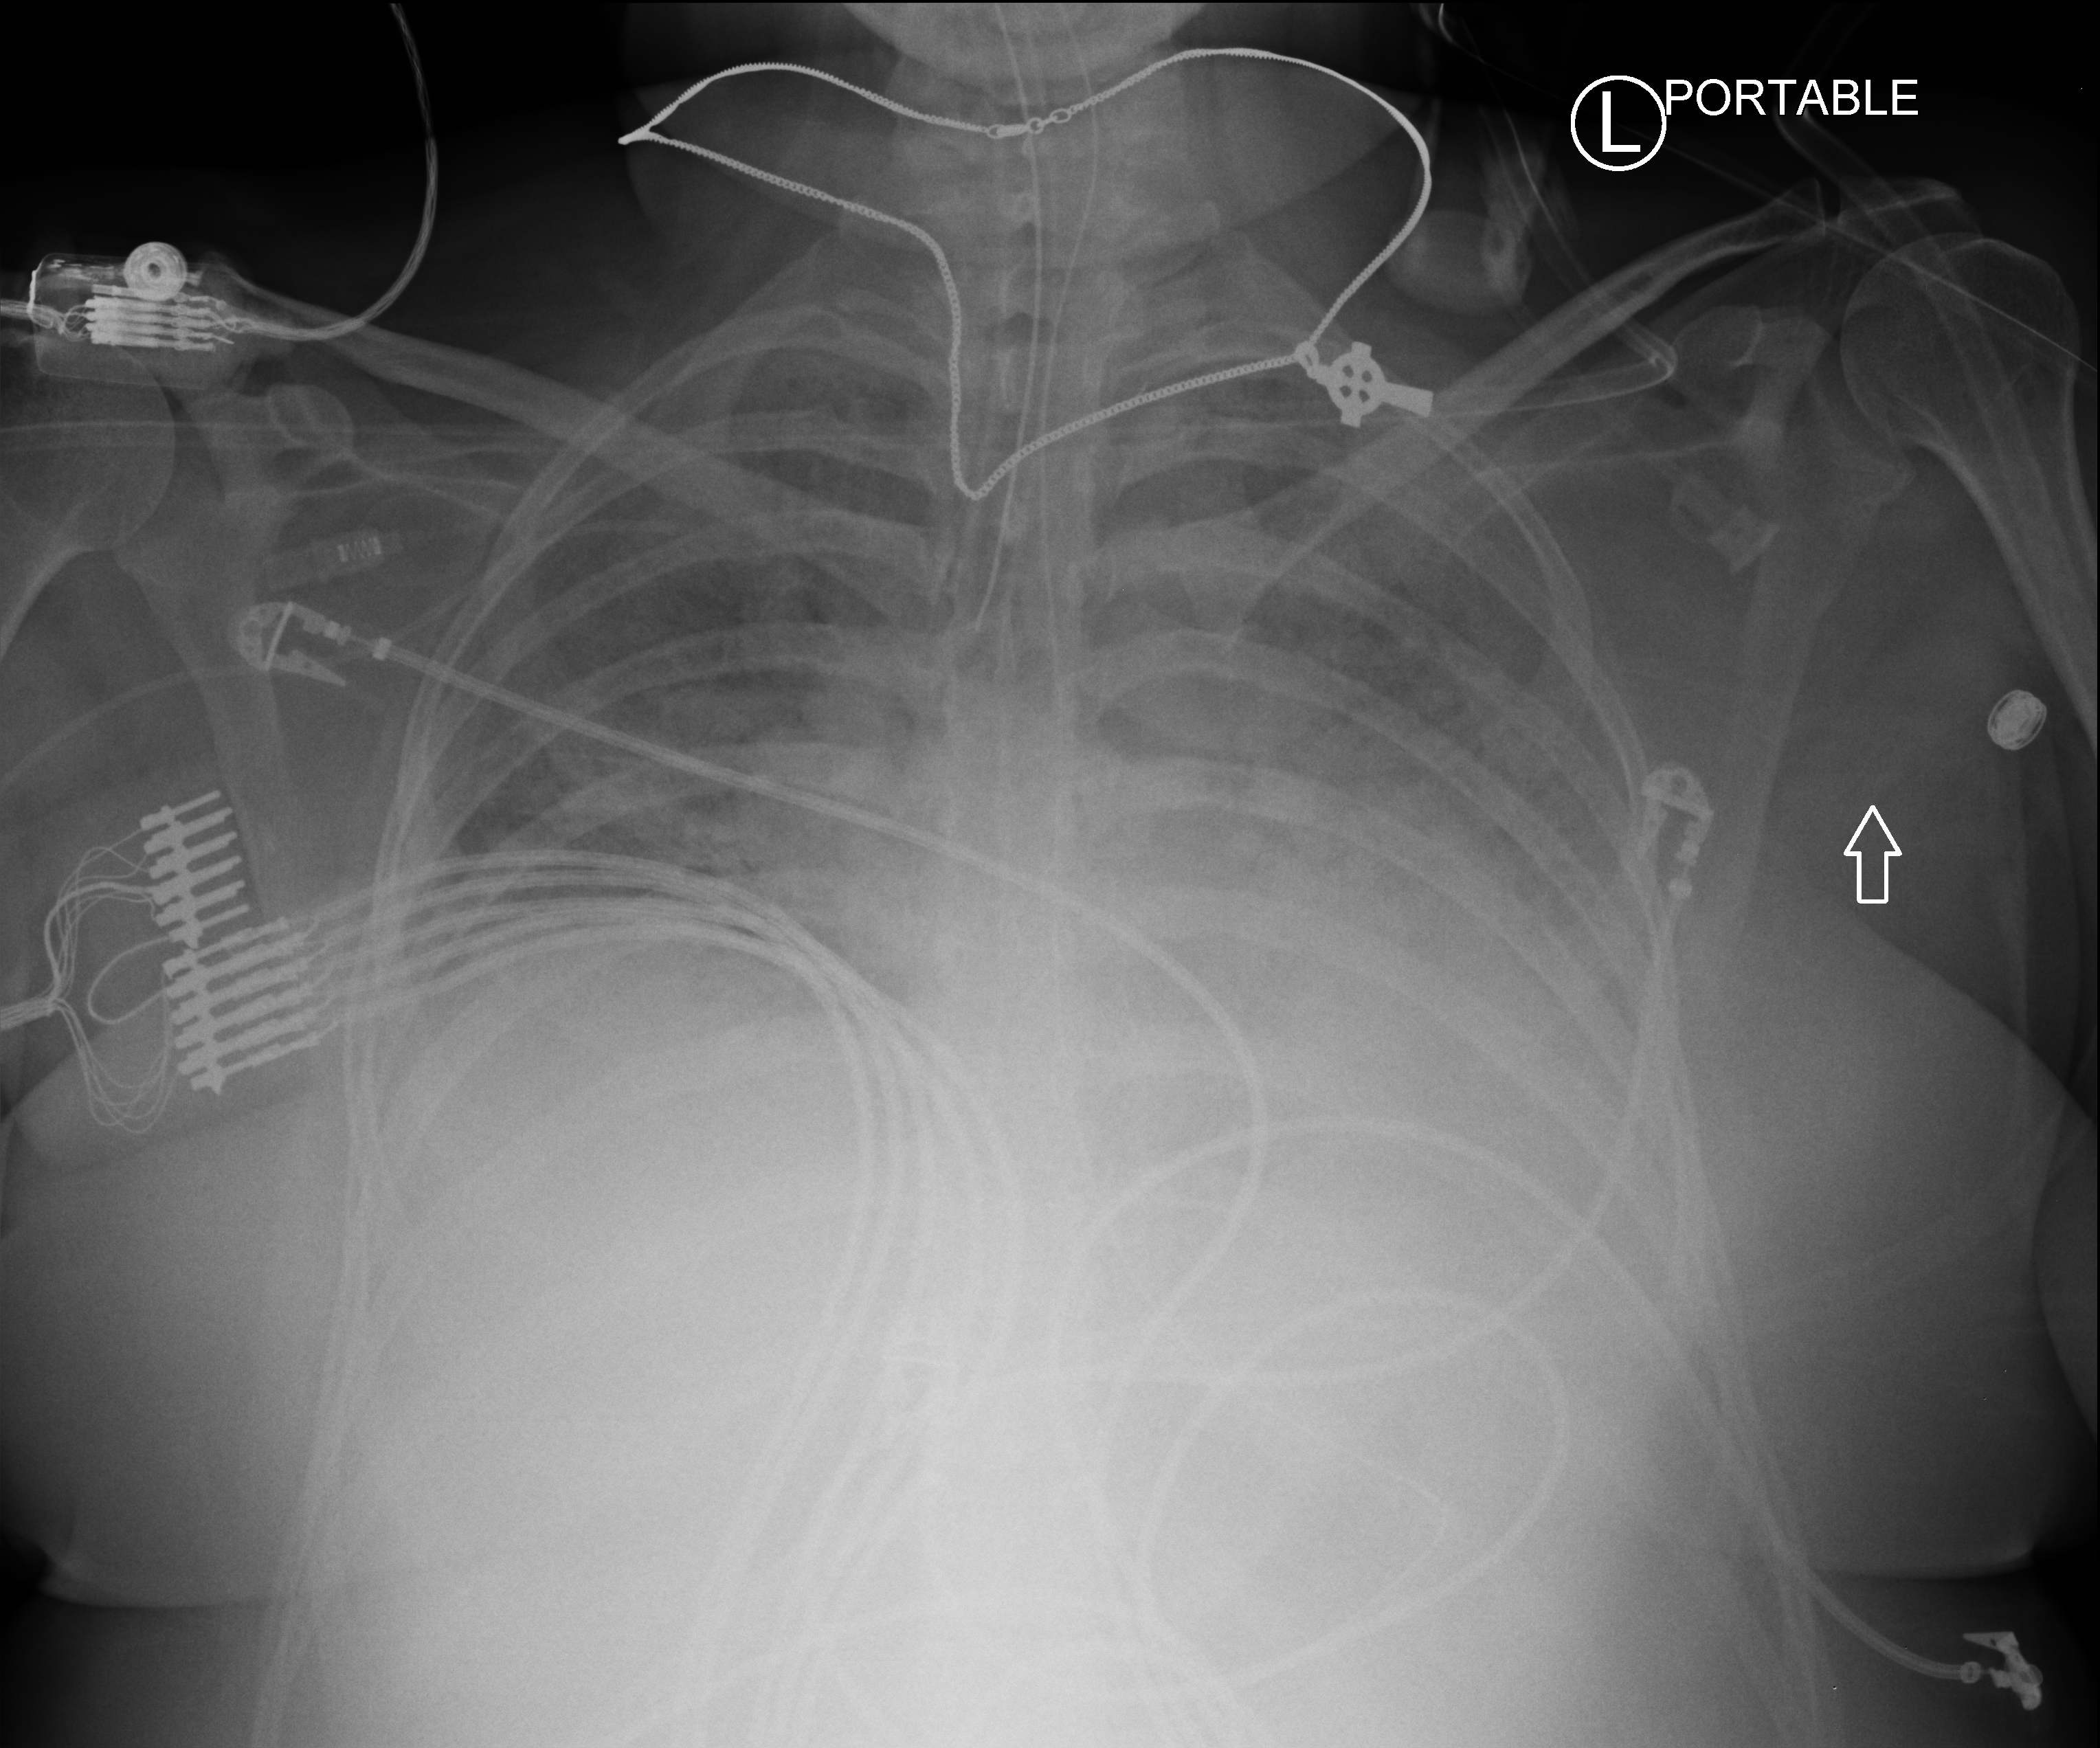
Portable chest radiograph; anteroposterior (AP) projection. Patient hospitalised with COVID-19; female, aged 18–59 years.
Hospital-stay facts (about this admission, not read from this image; timing relative to this image not recorded): hypertension (admission record): no.